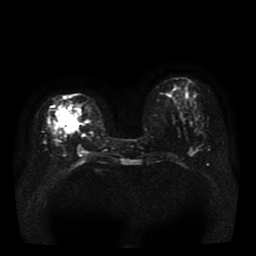
Breast MRI, one axial slice. Slice 15 of 41 in the series (ordered by position). Diffusion-weighted series; image 2 of 4 stored at this slice position (different b-values; order by instance number). 1.5 T. 5 mm slice thickness. 256 × 256 image matrix. Female patient.
Outlined on this slice (expert manual segmentation):
- tumour on diffusion-weighted imaging: box from (x=60, y=110) to (x=79, y=135) px